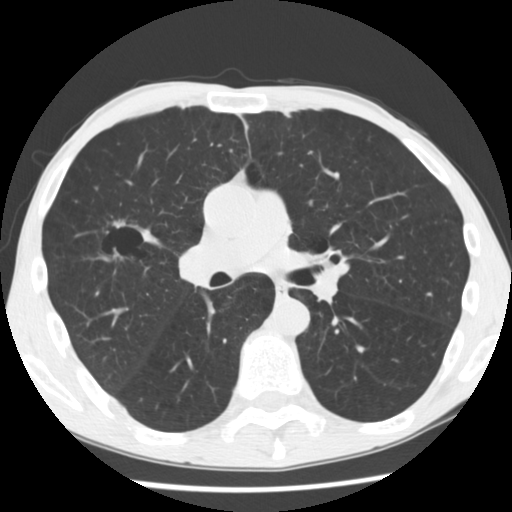
Low-dose screening chest CT, axial slice. First (baseline) screen. Lung window (W 1500 / L -600 HU). 2.5 mm slice thickness. Male, age 56 years at enrolment. Current smoker at enrolment.
• Lesion marked by an expert reader, bounding box (x1, y1, x2, y2) in pixels: (93, 205, 158, 261).
• The screening reader recorded 2 non-calcified nodules or masses ≥4 mm on this exam (right upper lobe, right upper lobe); which of them this box marks is not recorded.
• Participant outcome: lung cancer diagnosed 476 days after this screen (after the second annual screen) — squamous cell carcinoma, NOS, right upper lobe, right middle lobe, well differentiated (G1), stage IA (AJCC 6th edition), 27 mm at pathology.